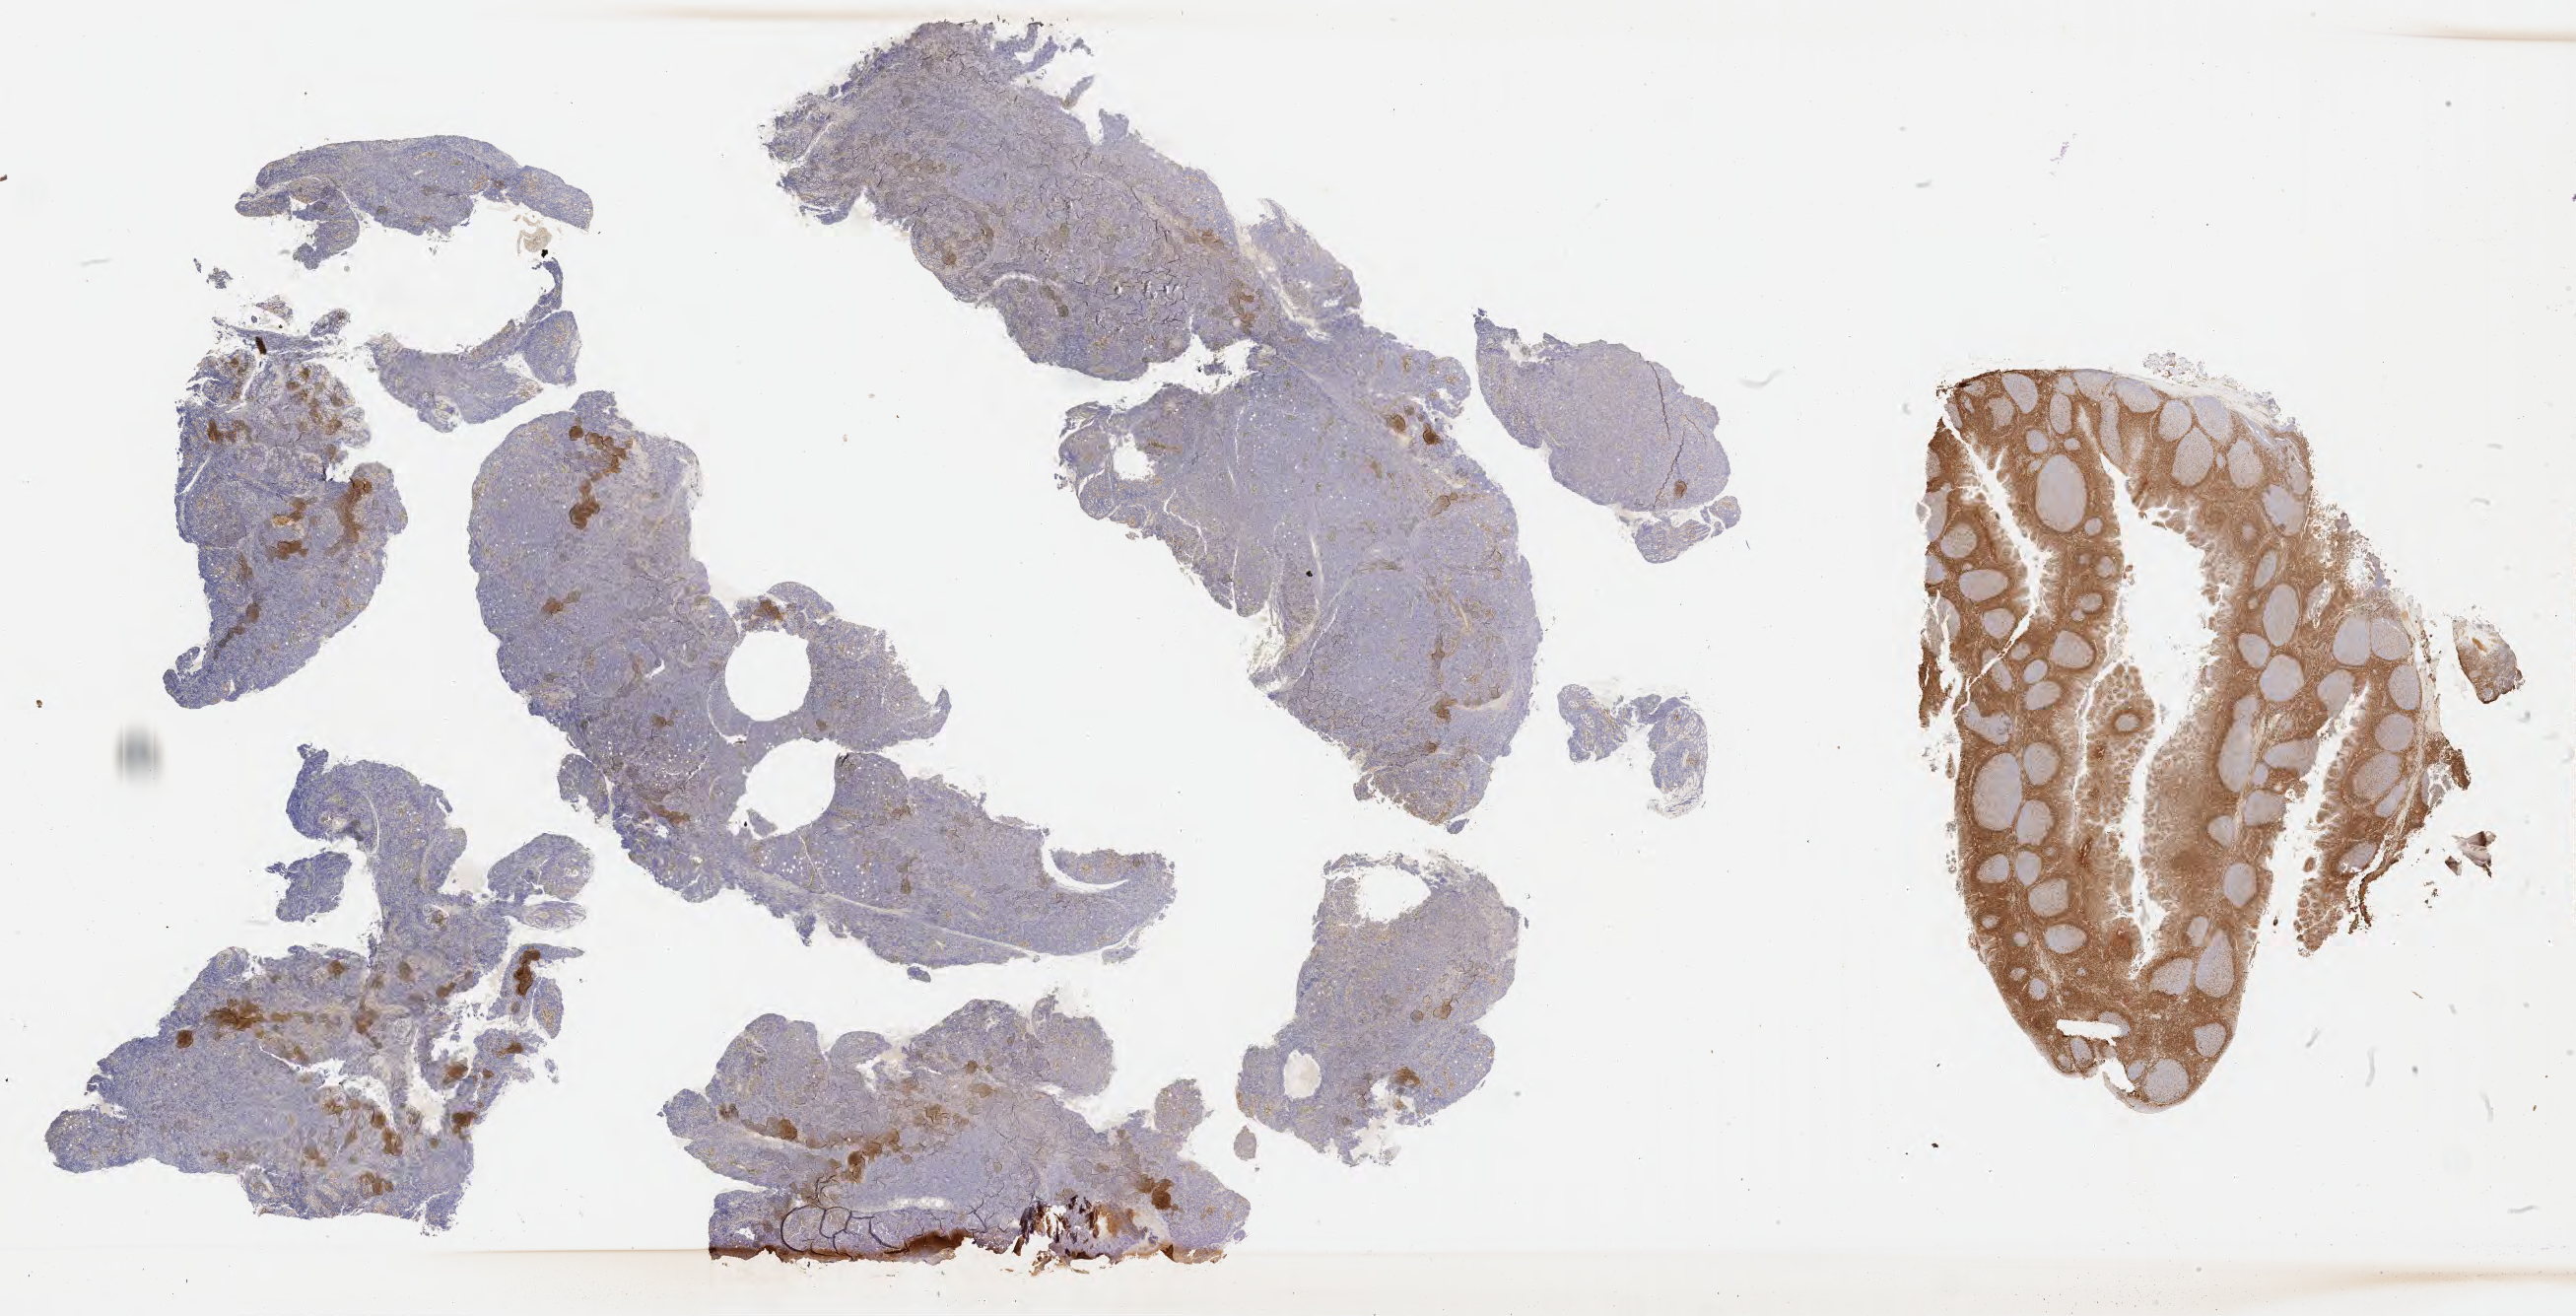
Immunohistochemistry (IHC) whole-slide image stained for BCL2, a low-resolution overview of the entire scanned area, about 42.3 x 21.6 mm; tumor tissue; anatomic site: cranium. Male, age 5 years at initial diagnosis.
* diagnosis: Burkitt lymphoma, NOS